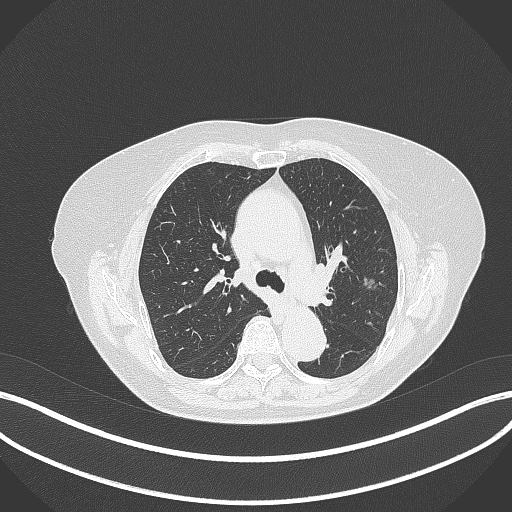
Chest CT, one axial slice; position 219 of 316 along the scan axis; reconstruction kernel B70f; lung window (W 1500 / L -600 HU); 512 × 512 image matrix, field of view 400 × 400 mm. Female patient, age 75 years. Case-level facts recorded for this patient, not image findings: clinical TNM (as recorded): T1c N0 M0.
Outlined on this slice (bounding box drawn by a radiologist):
- lung tumour (recorded histology: adenocarcinoma): bounding box <362,275,379,291> (left, top, right, bottom; pixels)